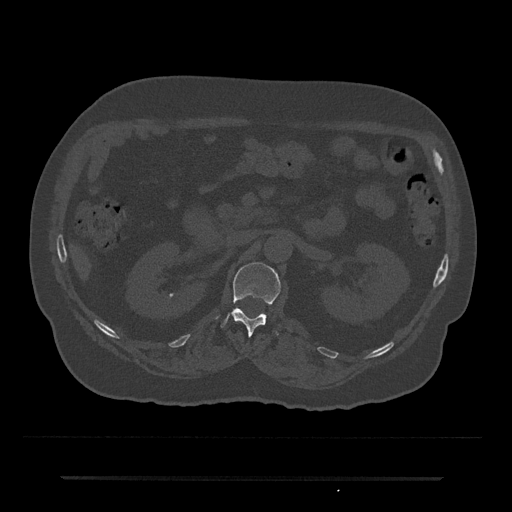
CT including the spine, one axial slice; position 68 of 797 along the scan axis; reconstruction kernel Br40s/3; 120 kVp; bone window (W 1800 / L 400 HU); 512 × 512 image matrix, field of view 437 × 437 mm. Male patient, age 69 years. From the clinical record (not read from this slice): primary cancer: prostate.
Structures marked on this image (semi-automatic segmentation, software-assisted and operator-edited):
- L1 vertebra: bounding box [x1, y1, x2, y2] px = [221, 262, 281, 336]